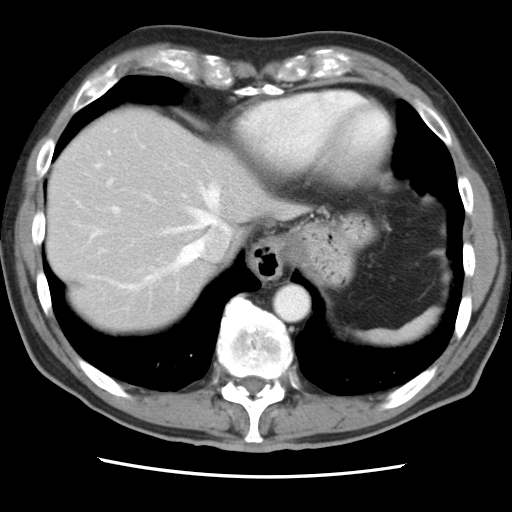
Contrast-enhanced abdominal CT, one axial slice; position 71 of 83 along the scan axis; soft-tissue window (W 400 / L 40 HU); 5 mm slice thickness; 512 × 512 image matrix. Male patient, age 69 years. Case-level facts recorded for this patient, not image findings: diagnosis: colorectal cancer liver metastases, imaged before liver resection; multiple liver metastases: yes; largest metastasis: 3.5 cm; chemotherapy before resection: yes.
Outlined on this slice (outlined manually by an expert reader):
- hepatic veins: bounding box (x1, y1, x2, y2) in pixels: (92, 130, 230, 290)
- liver: (48, 110, 292, 333)
- planned liver remnant (the part of the liver to remain after resection): (48, 149, 213, 332)
- portal vein (with intrahepatic branches): (102, 179, 187, 251)